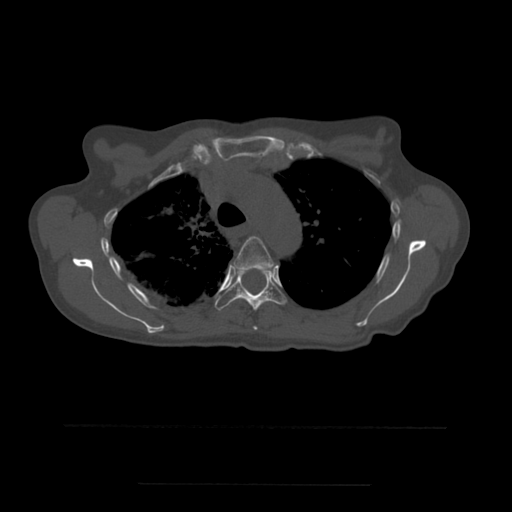
CT including the spine, one axial slice. Slice 398 of 544 in the series (ordered by position). Bone window (W 1800 / L 400 HU). 512 × 512 image matrix, field of view 350 × 350 mm. Patient age 58 years. From the clinical record (not read from this slice): primary cancer: lung.
Outlined on this slice (semi-automatic segmentation, software-assisted and operator-edited):
- T4 vertebra: box from (x=234, y=237) to (x=275, y=330) px
- T5 vertebra: (x=215, y=268)–(x=286, y=311)